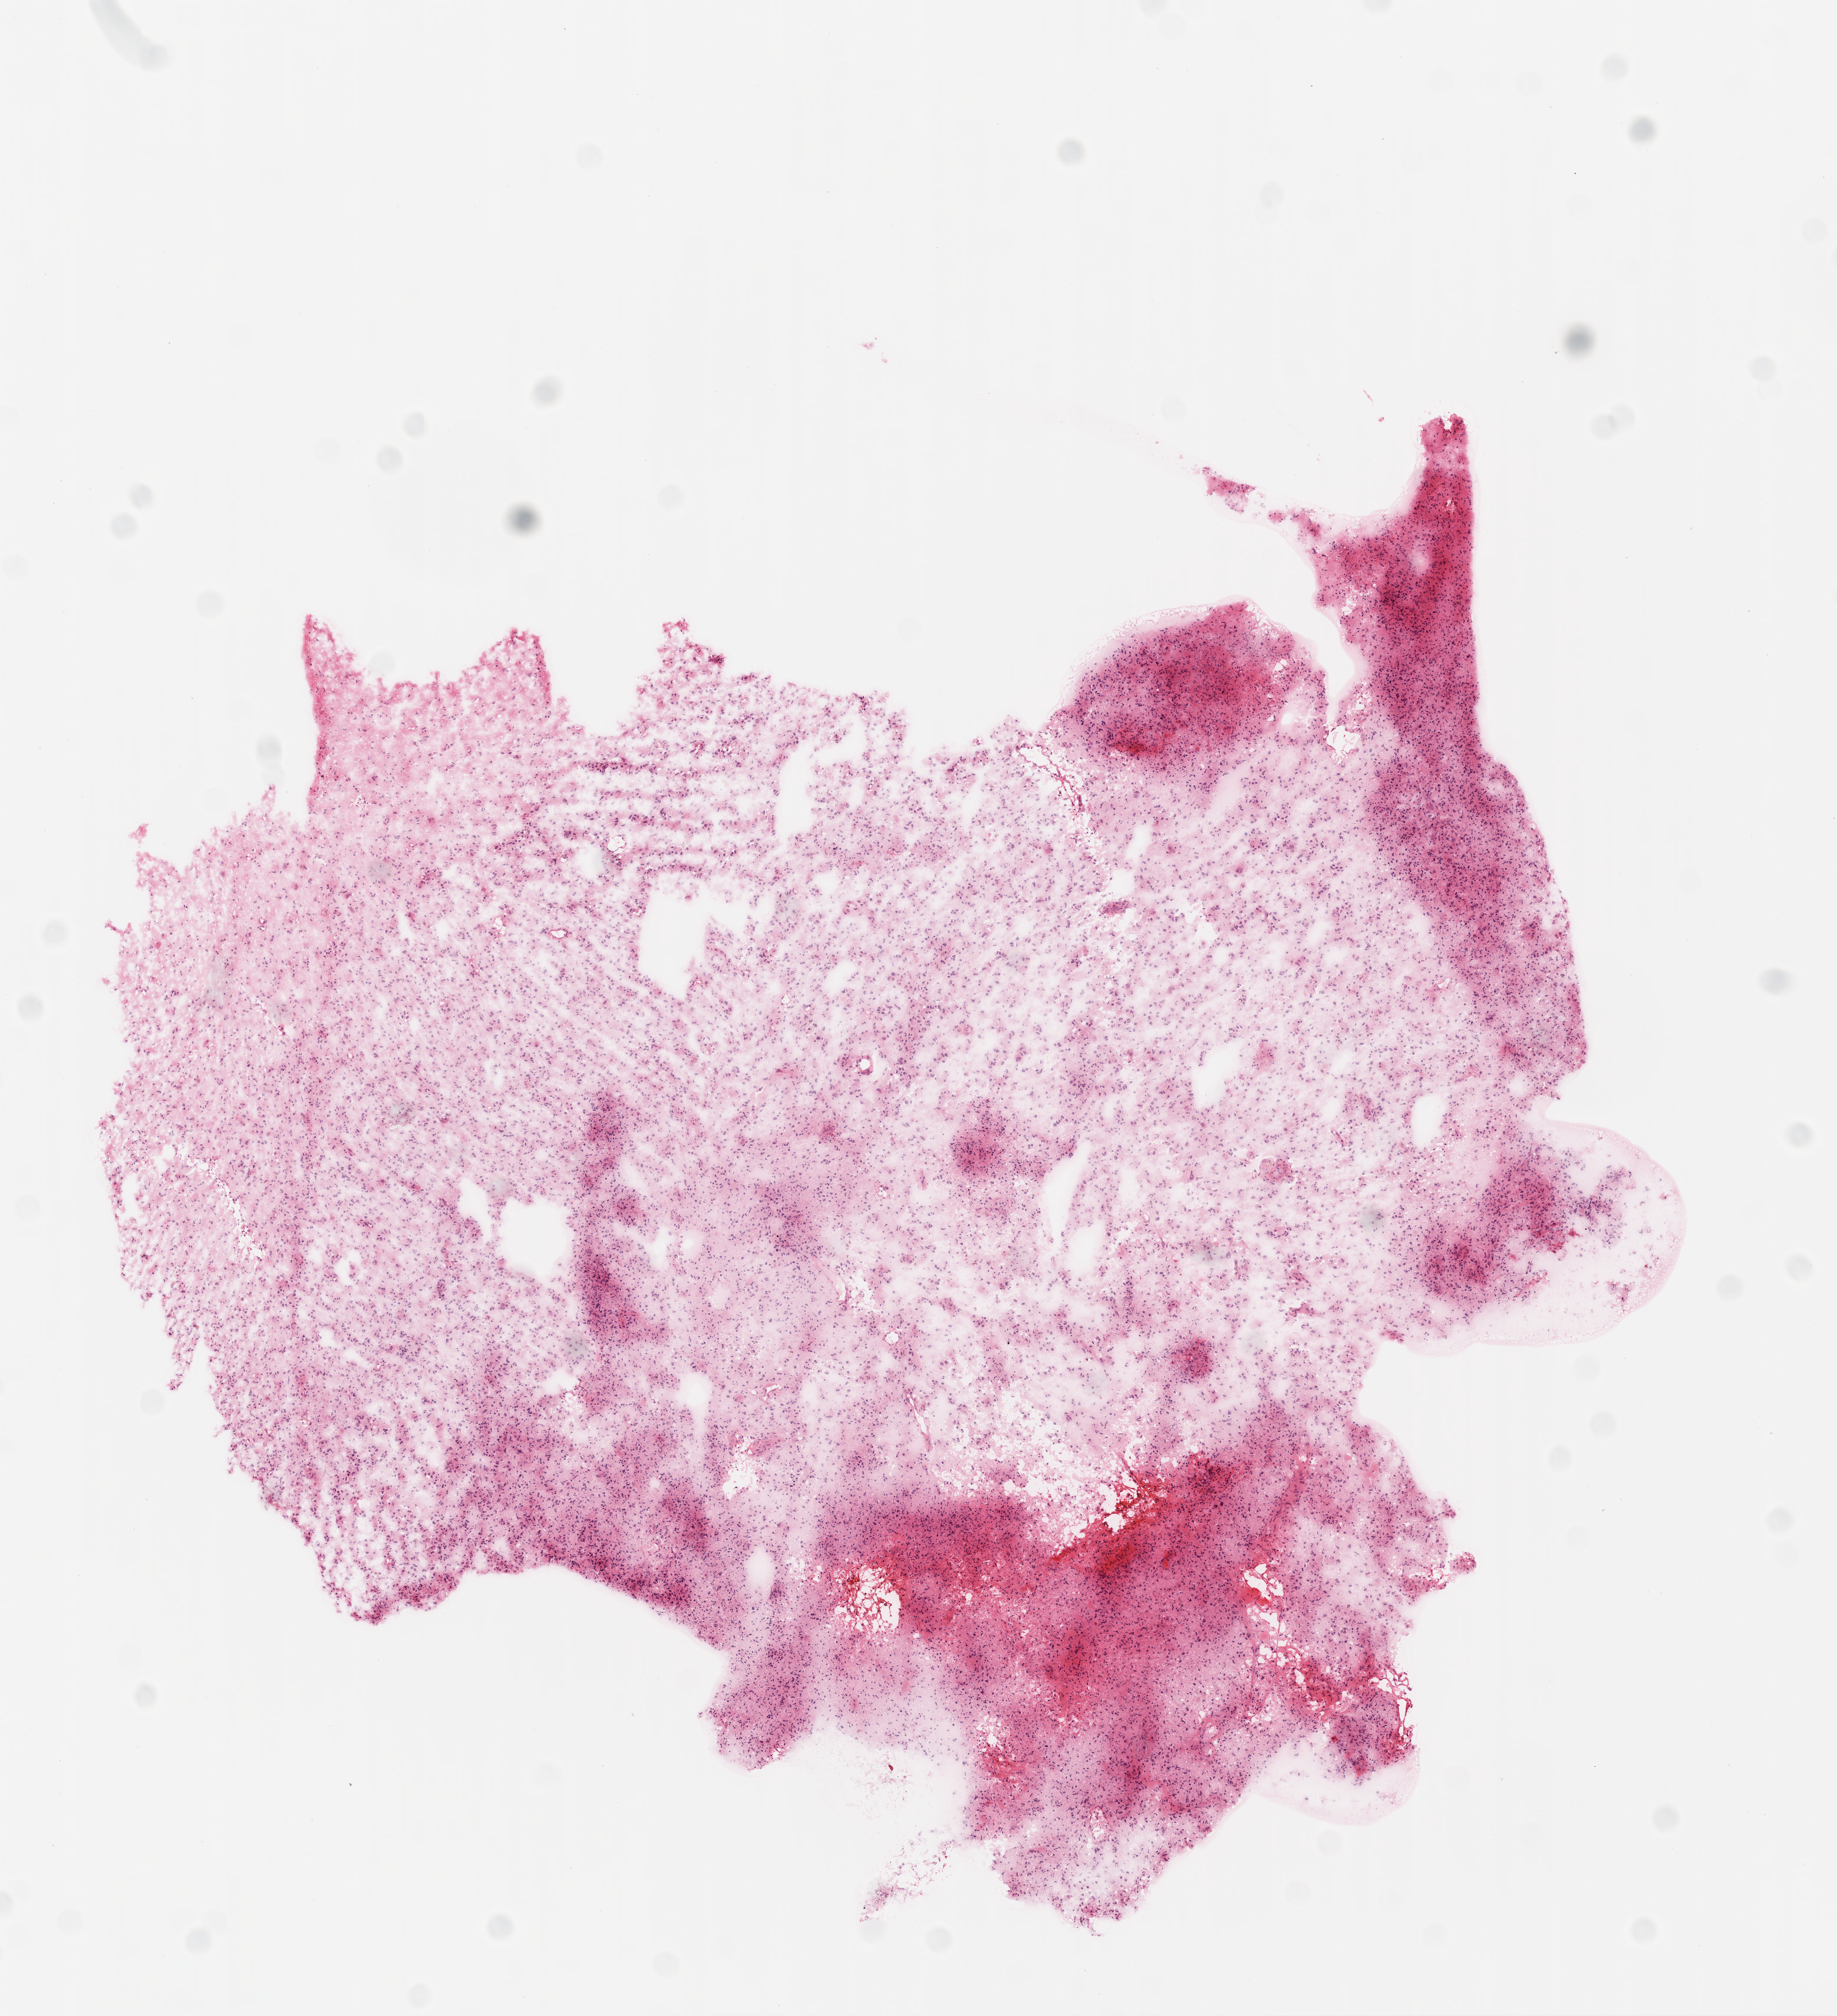
Whole-slide histology image, H&E-stained, whole scanned area (about 6.3 x 6.9 mm, slide scanned at 20x) shown as a low-resolution overview; frozen section from the top of the tissue portion; primary tumour sample from the brain. Patient: male, age at initial diagnosis 50 years. Pathologist review of this section (percent, as recorded): tumour cells 80%, tumour nuclei 80%, normal cells 0%, stromal cells 20%, necrosis 0%.
Pathologic diagnosis: Glioblastoma.